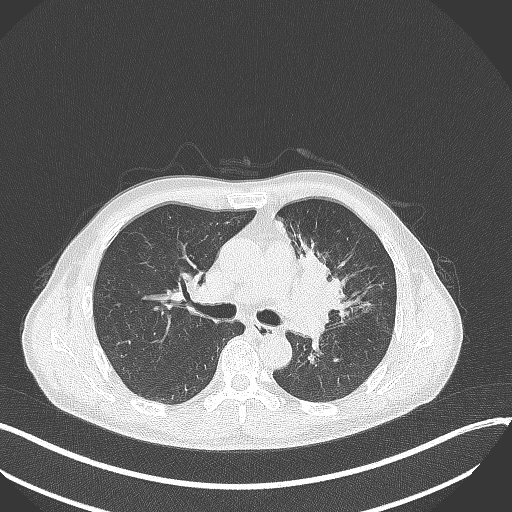
Chest CT, one axial slice; slice 205 of 411 in the series (ordered by position); reconstruction kernel B70f; lung window (W 1500 / L -600 HU); 1 mm slice thickness; 512 × 512 image matrix. Patient: male, 56 years. Case-level facts recorded for this patient, not image findings: clinical TNM (as recorded): T2a N0 M0.
Outlined on this slice (bounding box drawn by a radiologist):
- lung tumour (recorded histology: squamous cell carcinoma): box from (x=287, y=249) to (x=362, y=330) px